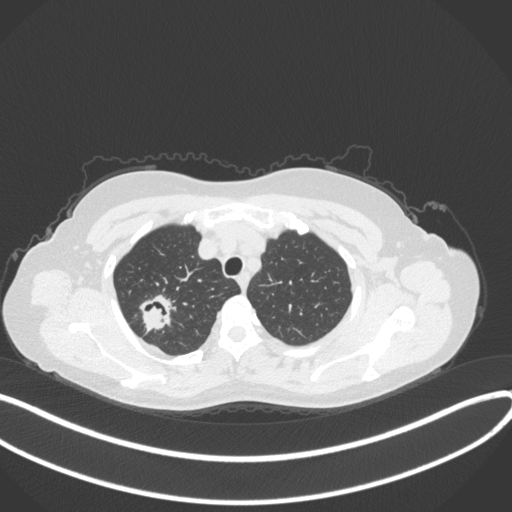
Chest CT, one axial slice. Position 301 of 342 along the scan axis. 120 kVp. Lung window (W 1500 / L -600 HU). 1 mm slice thickness. 512 × 512 image matrix, field of view 400 × 400 mm. Female patient, age 50 years. From the clinical record (not read from this slice): clinical TNM (as recorded): T1c N0 M0; histopathological grade: G2-3.
Outlined on this slice (rectangle marked by the reading radiologist):
- lung tumour (recorded histology: adenocarcinoma): bounding box (x1, y1, x2, y2) in pixels: (134, 289, 177, 336)